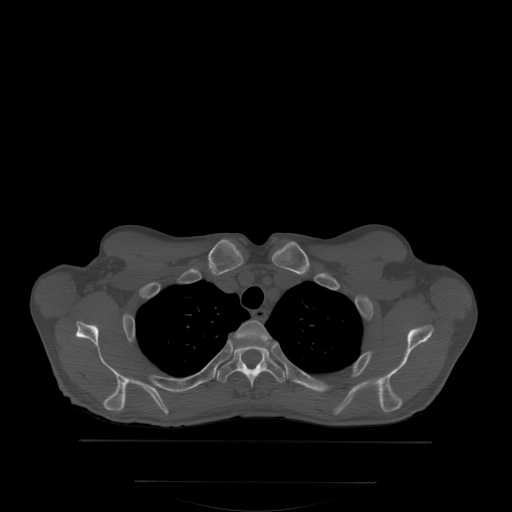
CT including the spine, one axial slice. Position 271 of 350 along the scan axis. Bone window (W 1800 / L 400 HU). 2.5 mm slice thickness. 512 × 512 image matrix, field of view 500 × 500 mm. Patient: male, 58 years. Case-level facts recorded for this patient, not image findings: primary cancer: prostate; vertebrae with lytic lesions (as recorded): L1.
Structures marked on this image (semi-automatic segmentation, software-assisted and operator-edited):
- T2 vertebra: bounding box (x1, y1, x2, y2) in pixels: (211, 320, 267, 363)
- T3 vertebra: (216, 336, 286, 385)